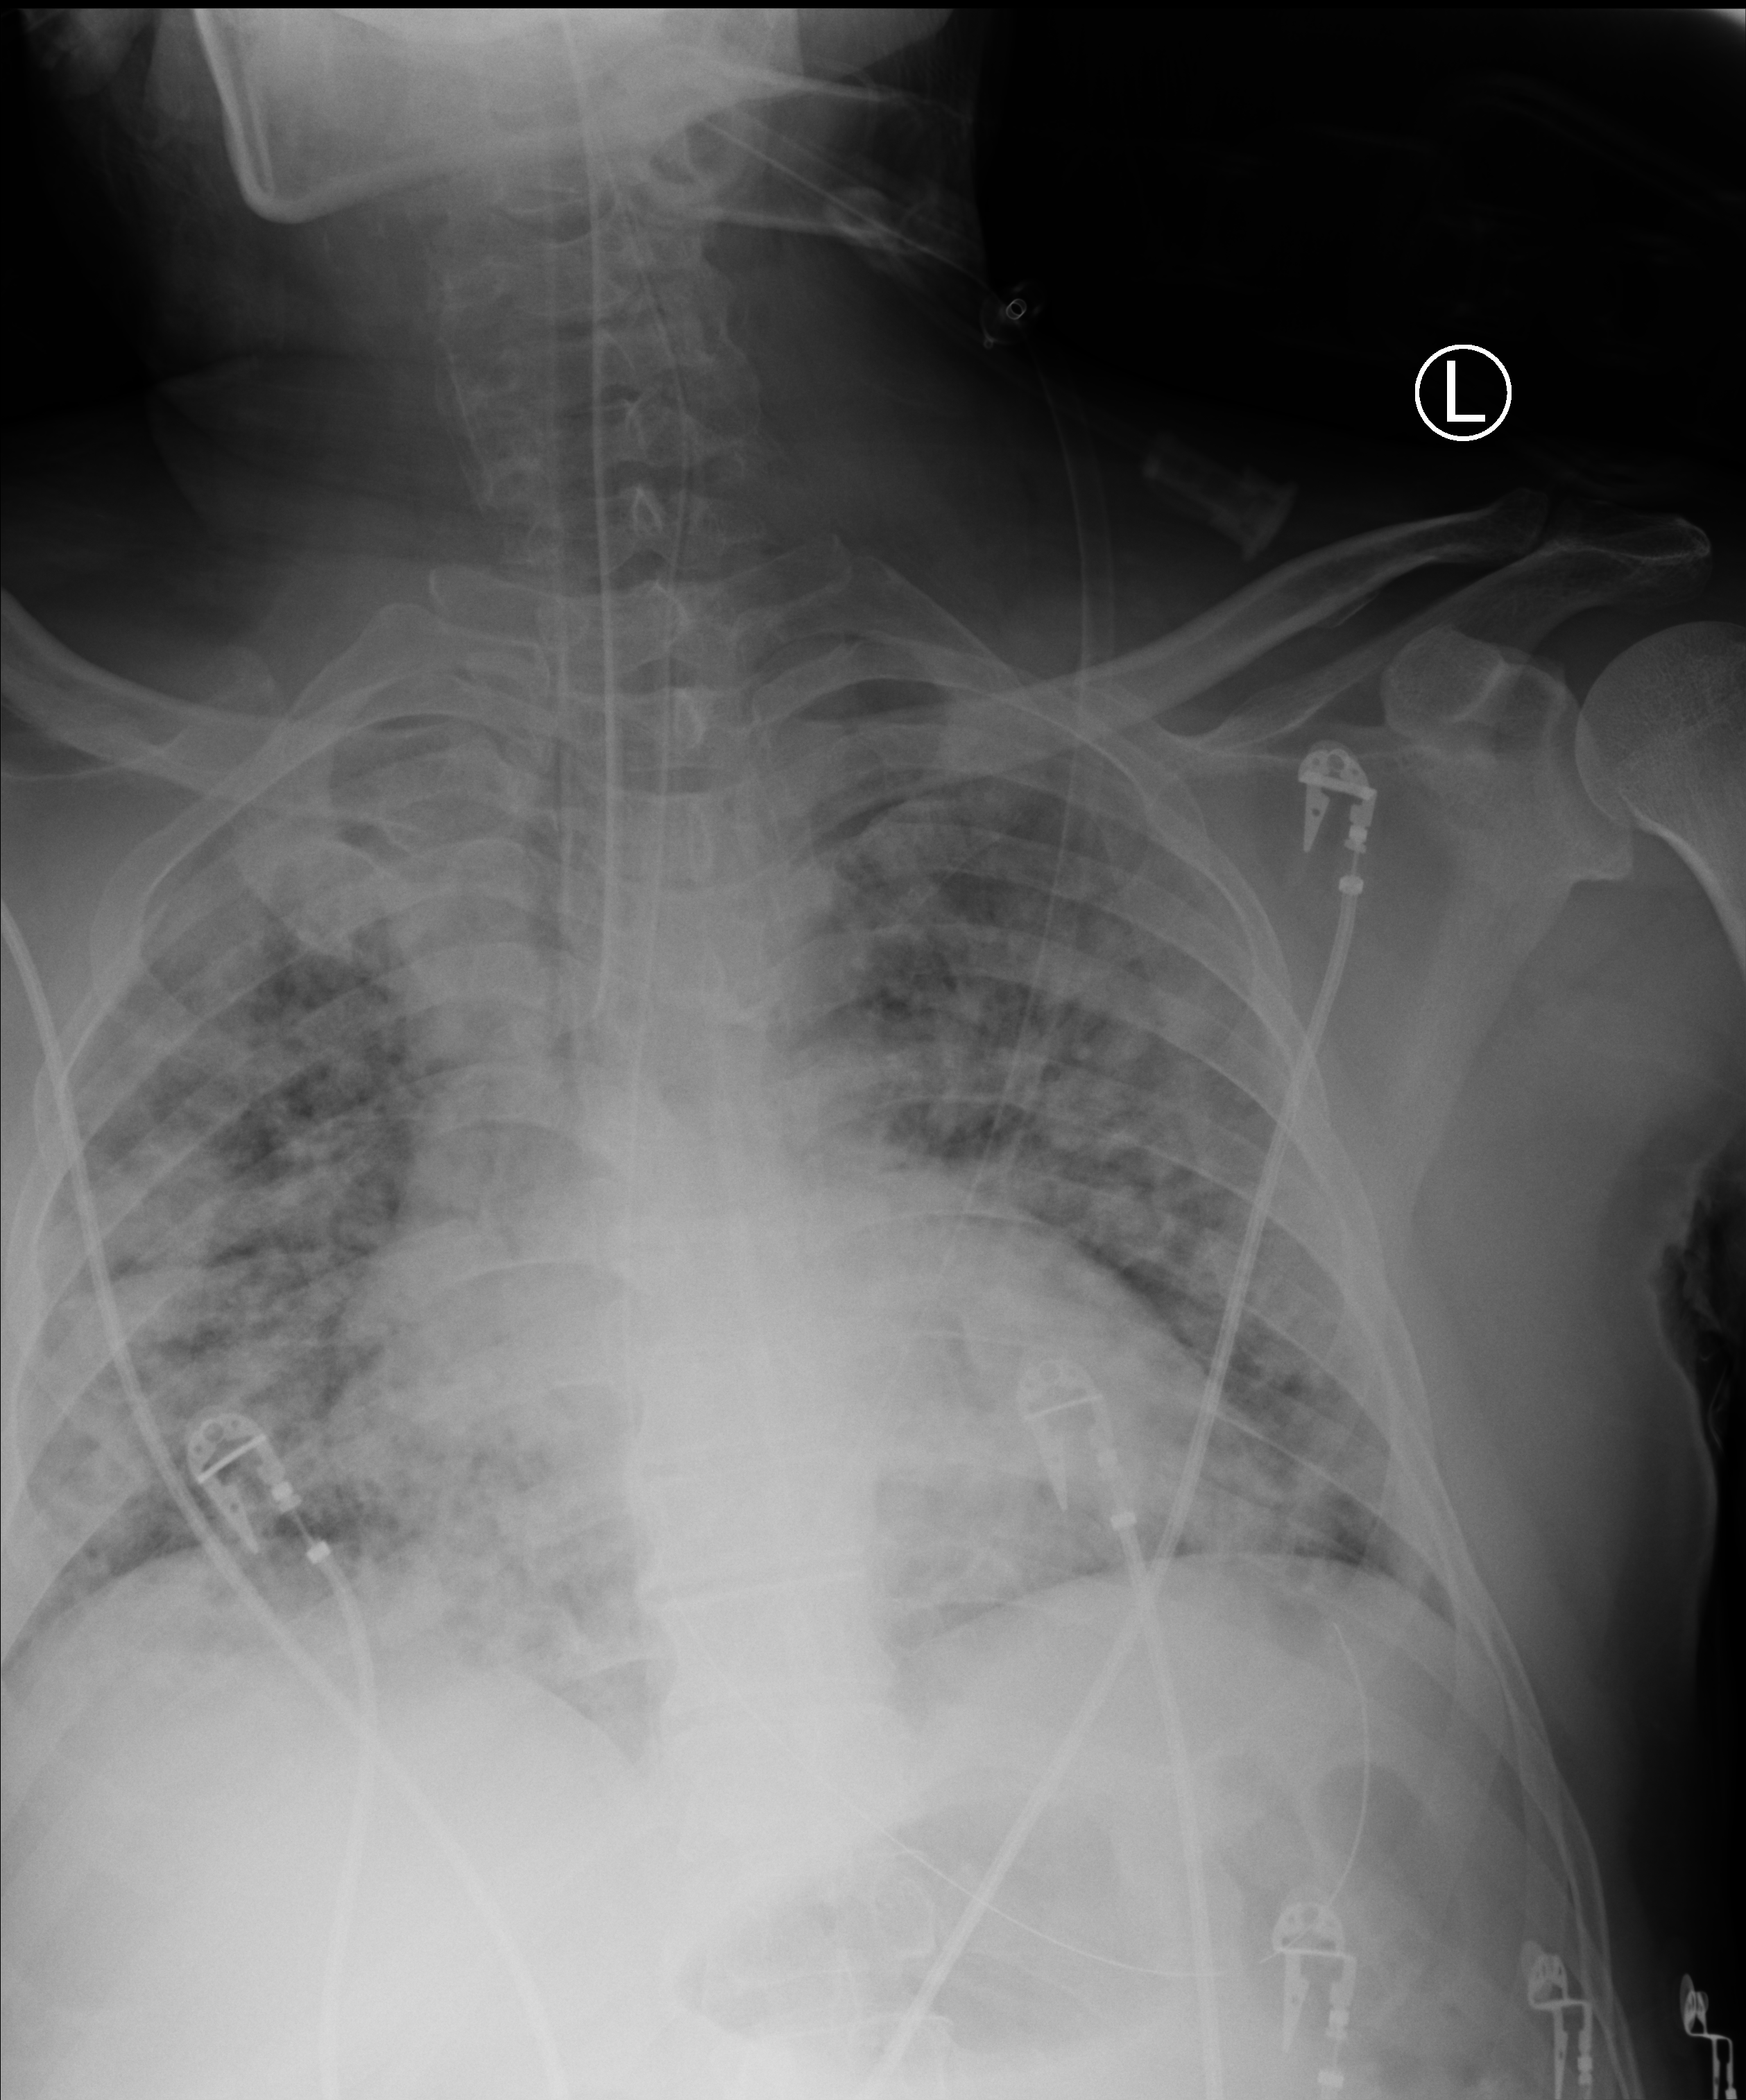
Chest X-ray (portable); anteroposterior (AP) projection. Male patient hospitalised with COVID-19, age 18–59 years.
Admission-level facts for this patient (not findings on this image; timing relative to this image not recorded): mechanically ventilated during this hospital stay: yes.